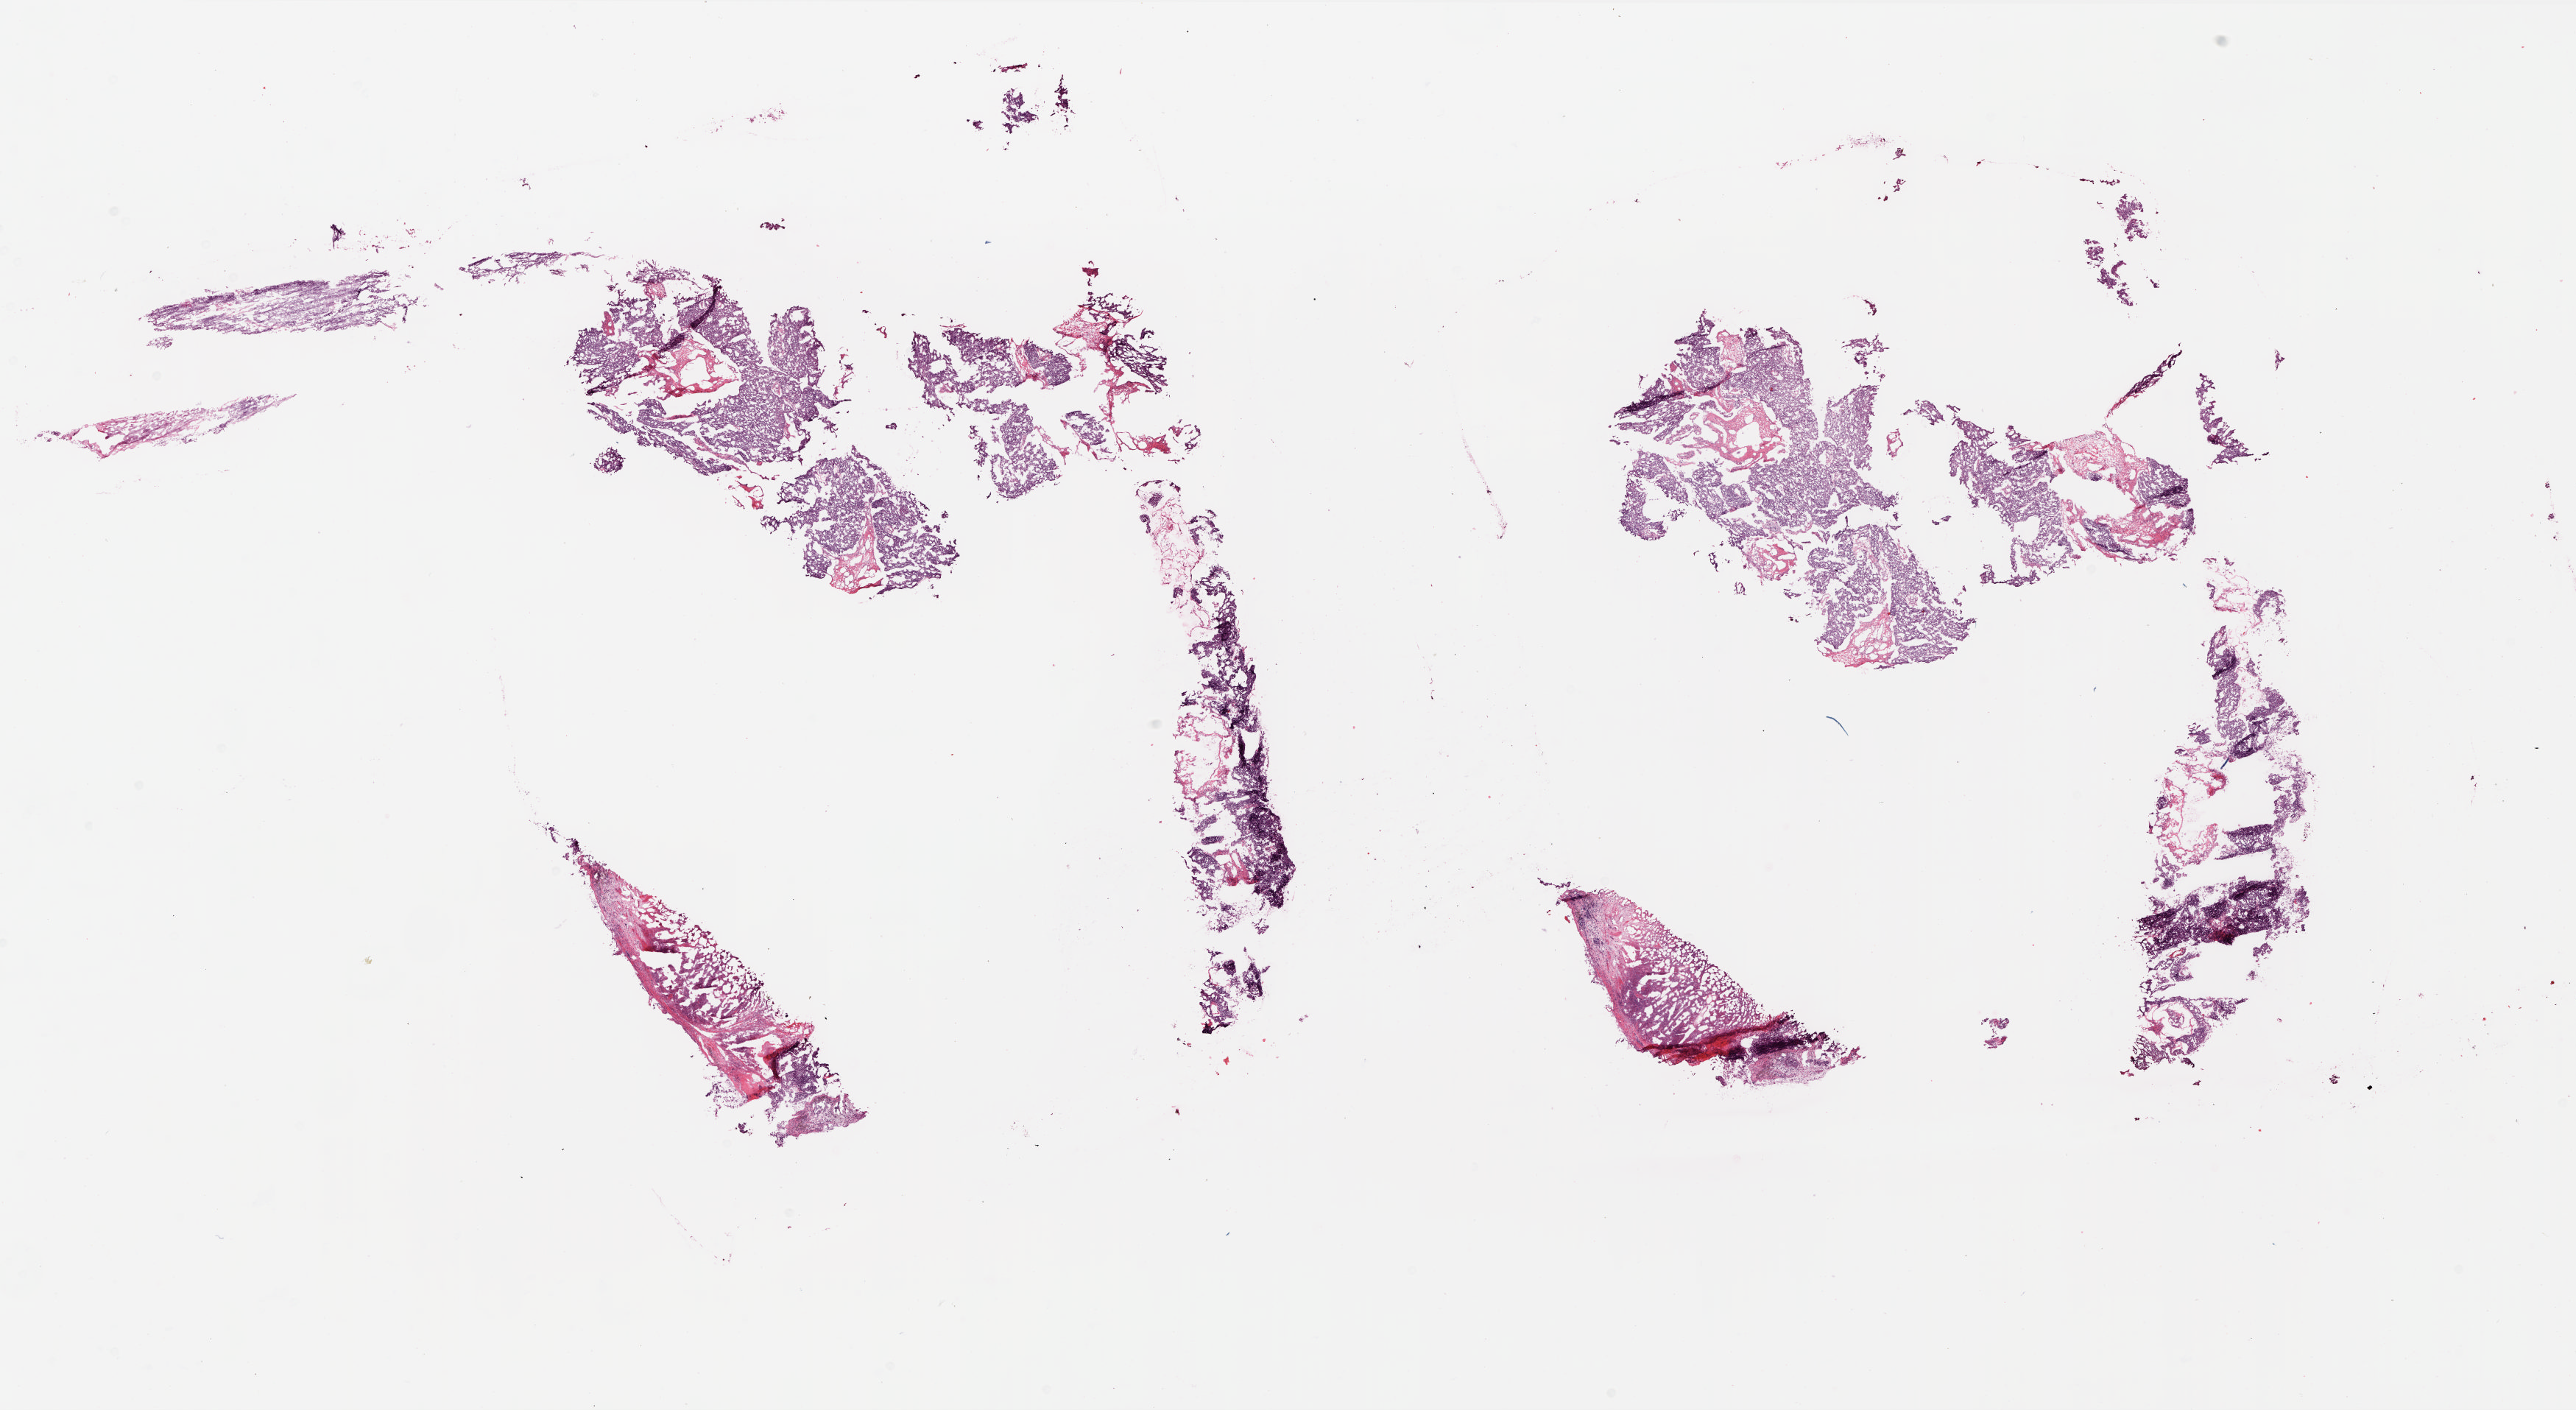
Digitized H&E tissue section (whole slide), low-resolution overview of the scanned area, about 27.9 x 15.3 mm. Frozen section from the top of the tissue portion. Primary tumour sample from the ovary. Female patient; age at initial diagnosis 50 years. Histologic grade: G3 (poorly differentiated). Composition of this section per pathologist review: tumour cells 88%, tumour nuclei 95%, normal cells 0%, stromal cells 10%, necrosis 2%.
Pathologic diagnosis: Serous cystadenocarcinoma, NOS. Laterality: bilateral. FIGO stage: IIIC.